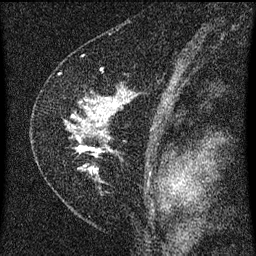
Breast MRI (dynamic contrast-enhanced), one sagittal slice. Slice 41 of 60 in the series (ordered by position). Dynamic contrast-enhanced series, image 2 of 3 at this slice position (ordered by acquisition). 1.5 T. TE 4.2 ms, TR 8 ms. 2 mm slice thickness. 256 × 256 image matrix, field of view 180 × 180 mm. Patient: female, 47 years.
Outlined on this slice (semi-automatic segmentation, software-assisted and operator-edited):
- analysis volume of interest (the breast-tissue region the enhancement analysis was run in; not a lesion): bounding box [x1, y1, x2, y2] px = [40, 86, 133, 191]
- tumour enhancement mask (voxels above the 70 % enhancement threshold inside the analysis volume of interest): [77, 104, 114, 173]